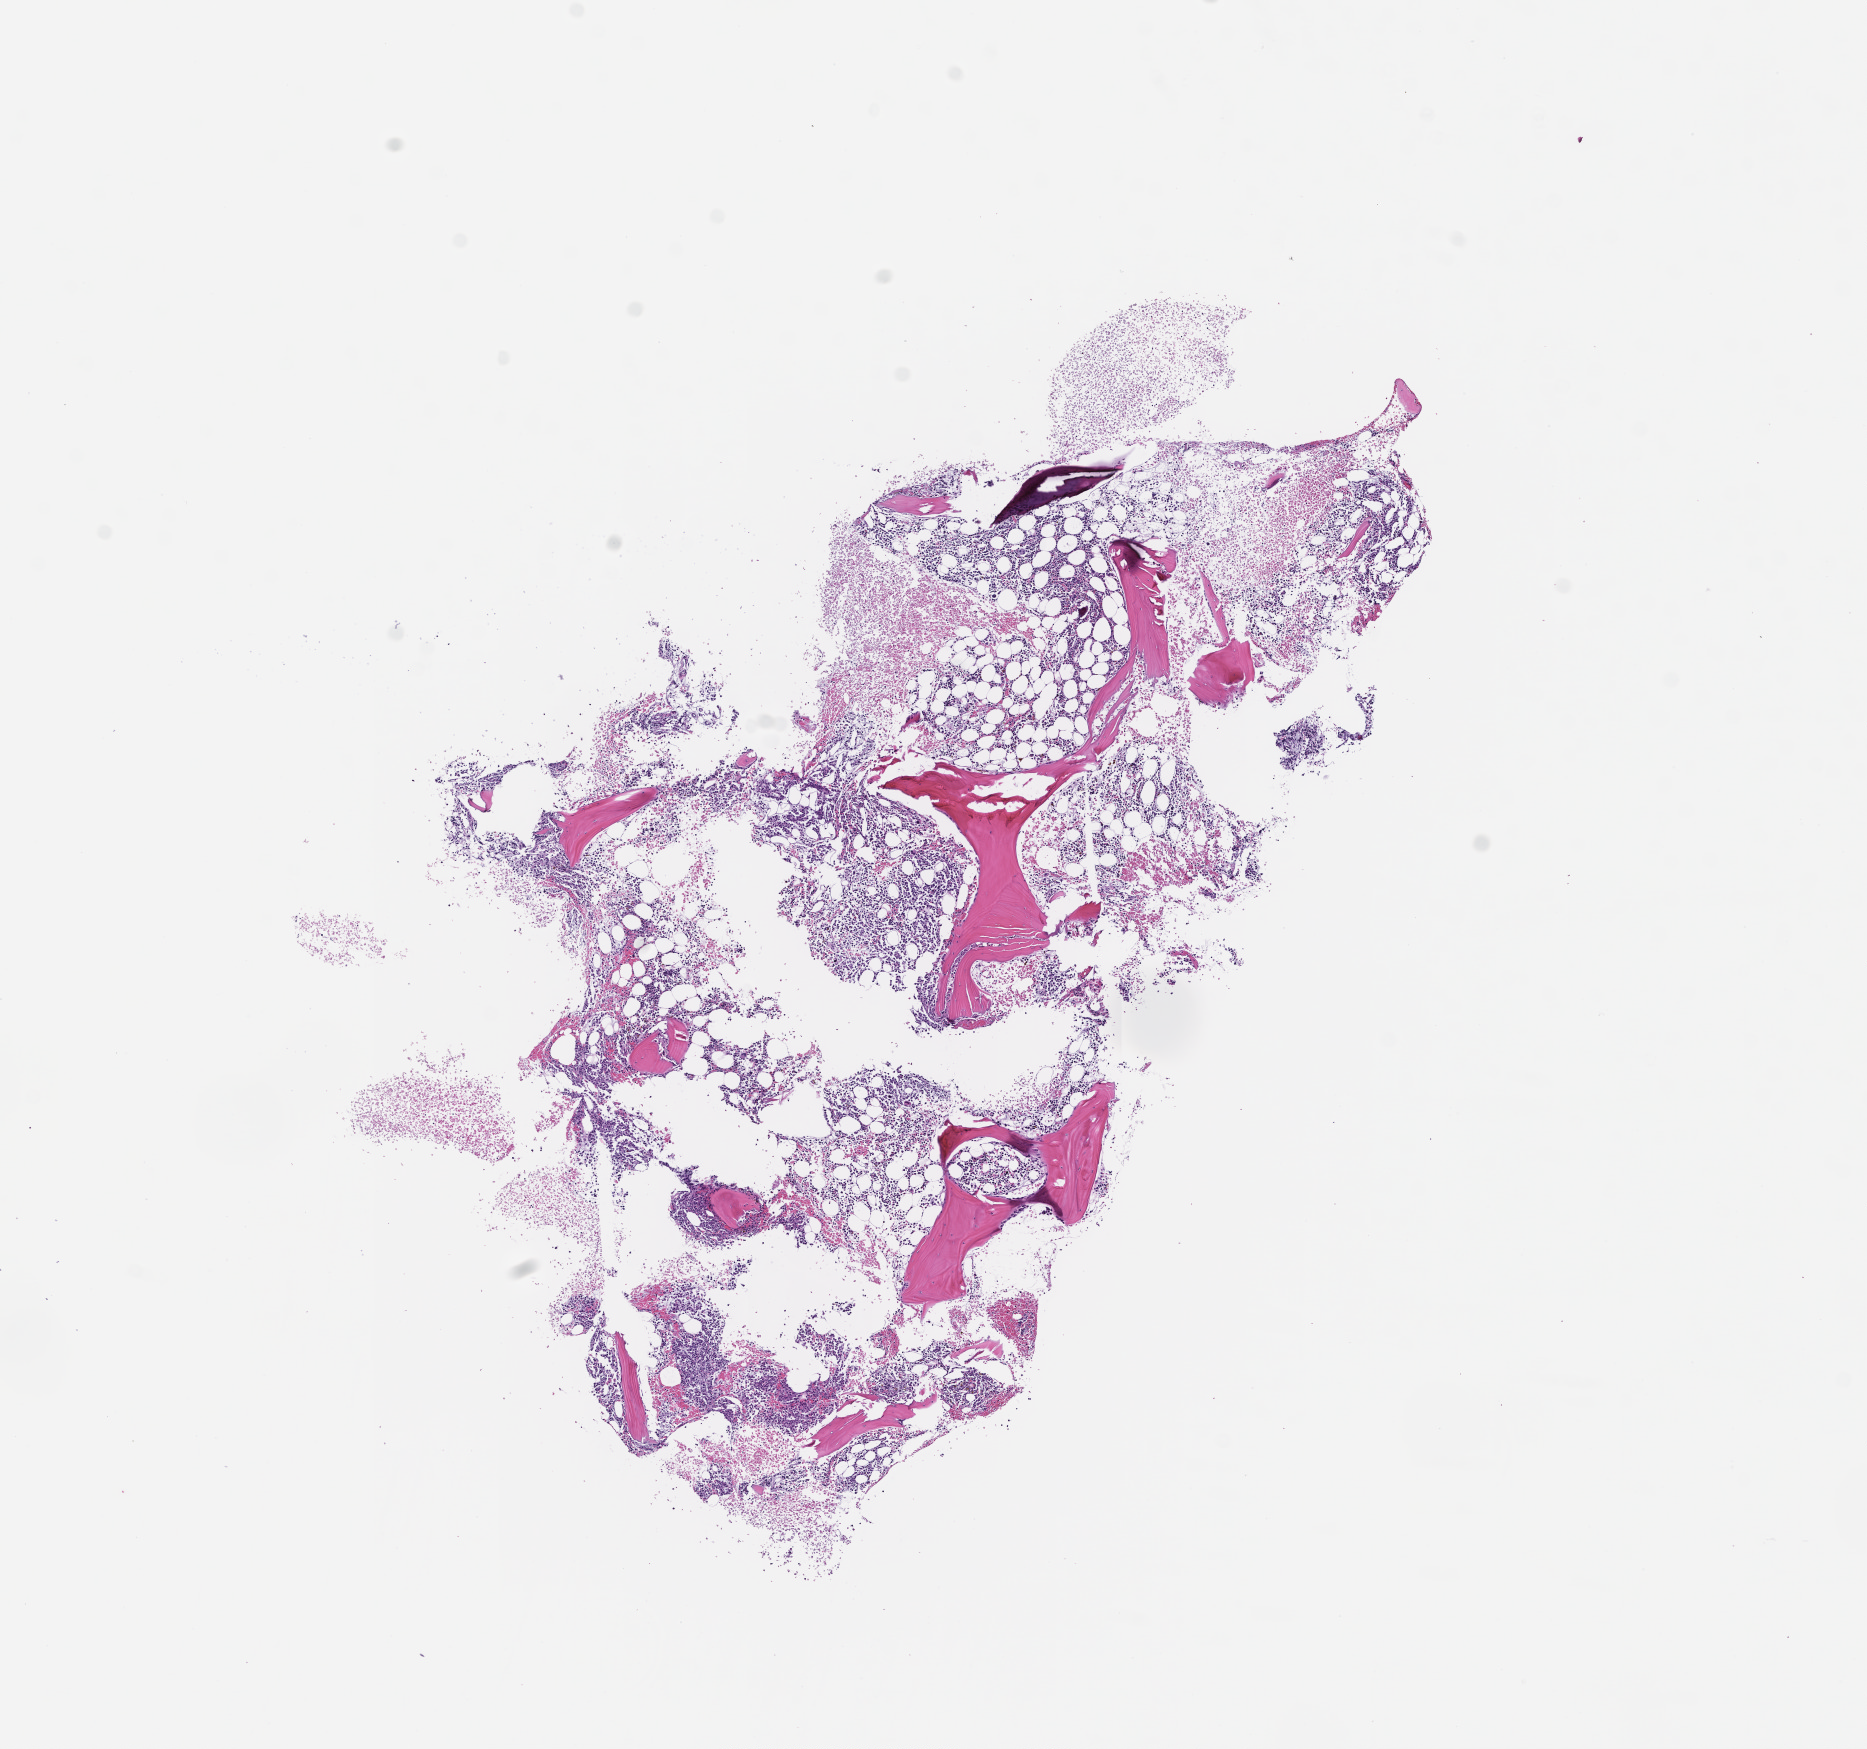
Whole-slide image, haematoxylin and eosin stain — a low-resolution overview of the entire scanned area, about 7.5 x 7.1 mm; formalin-fixed, paraffin-embedded (FFPE) tissue; tissue site: bone marrow; collected on treatment. Patient sex: male.
This section: primary tumour tissue. Diagnosis: Plasma Cell Myeloma.